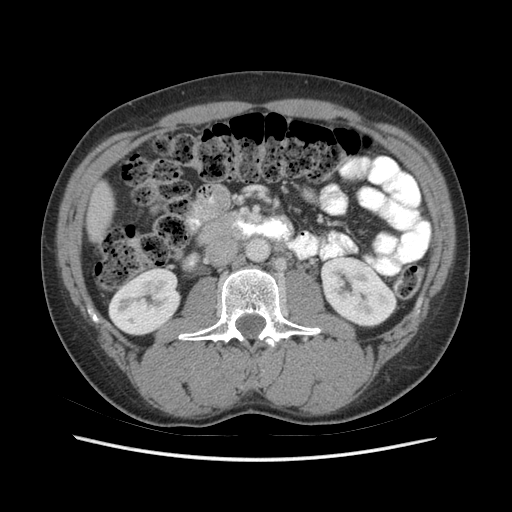
Contrast-enhanced abdominal CT (liver protocol), one axial slice; position 10 of 73 along the scan axis; reconstruction kernel STANDARD; soft-tissue window (W 400 / L 40 HU); 2.5 mm slice thickness; 512 × 512 image matrix. From the clinical record (not read from this slice): diagnosis: hepatocellular carcinoma (patient treated with transarterial chemoembolisation; whether this scan precedes or follows treatment is not stated here); TNM stage (as recorded): Stage-IIIA; Child-Pugh class: A; tumour nodularity: multinodular; tumour size: 6.6 cm.
Outlined on this slice (semi-automatic segmentation, software-assisted and operator-edited):
- liver parenchyma outside the tumour (the mass and vessels are separate outlines, so this box may not span the whole liver): box from (x=86, y=182) to (x=114, y=242) px